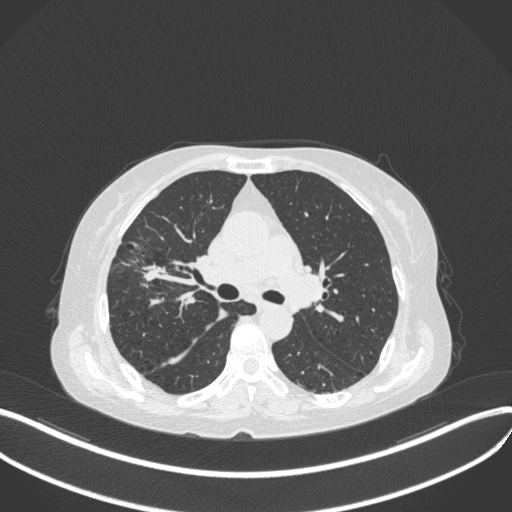
Chest CT, one axial slice. Position 249 of 429 along the scan axis. Reconstruction kernel B31f. Lung window (W 1500 / L -600 HU). 1 mm slice thickness. 512 × 512 image matrix. Patient: female, 69 years. From the clinical record (not read from this slice): clinical TNM (as recorded): T1b N3 M0.
Structures marked on this image (rectangle marked by the reading radiologist):
- lung tumour (recorded histology: small cell carcinoma): bounding box (x1, y1, x2, y2) in pixels: (134, 256, 170, 285)